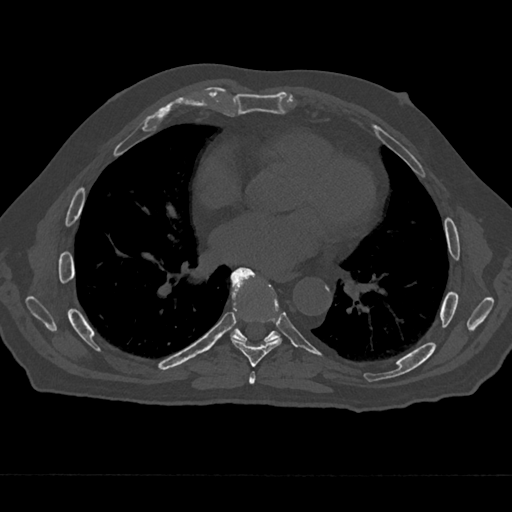
CT including the spine, one axial slice. Slice 351 of 797 in the series (ordered by position). Reconstruction kernel Br40s/3. 120 kVp. Bone window (W 1800 / L 400 HU). 0.5 mm slice thickness. 512 × 512 image matrix, field of view 377 × 377 mm. Male patient, age 75 years. From the clinical record (not read from this slice): primary cancer: renal.
Outlined on this slice (semi-automatic segmentation, software-assisted and operator-edited):
- T6 vertebra: box from (x=249, y=371) to (x=255, y=385) px
- T7 vertebra: (x=231, y=267)–(x=282, y=367)
- T8 vertebra: (x=230, y=274)–(x=280, y=343)